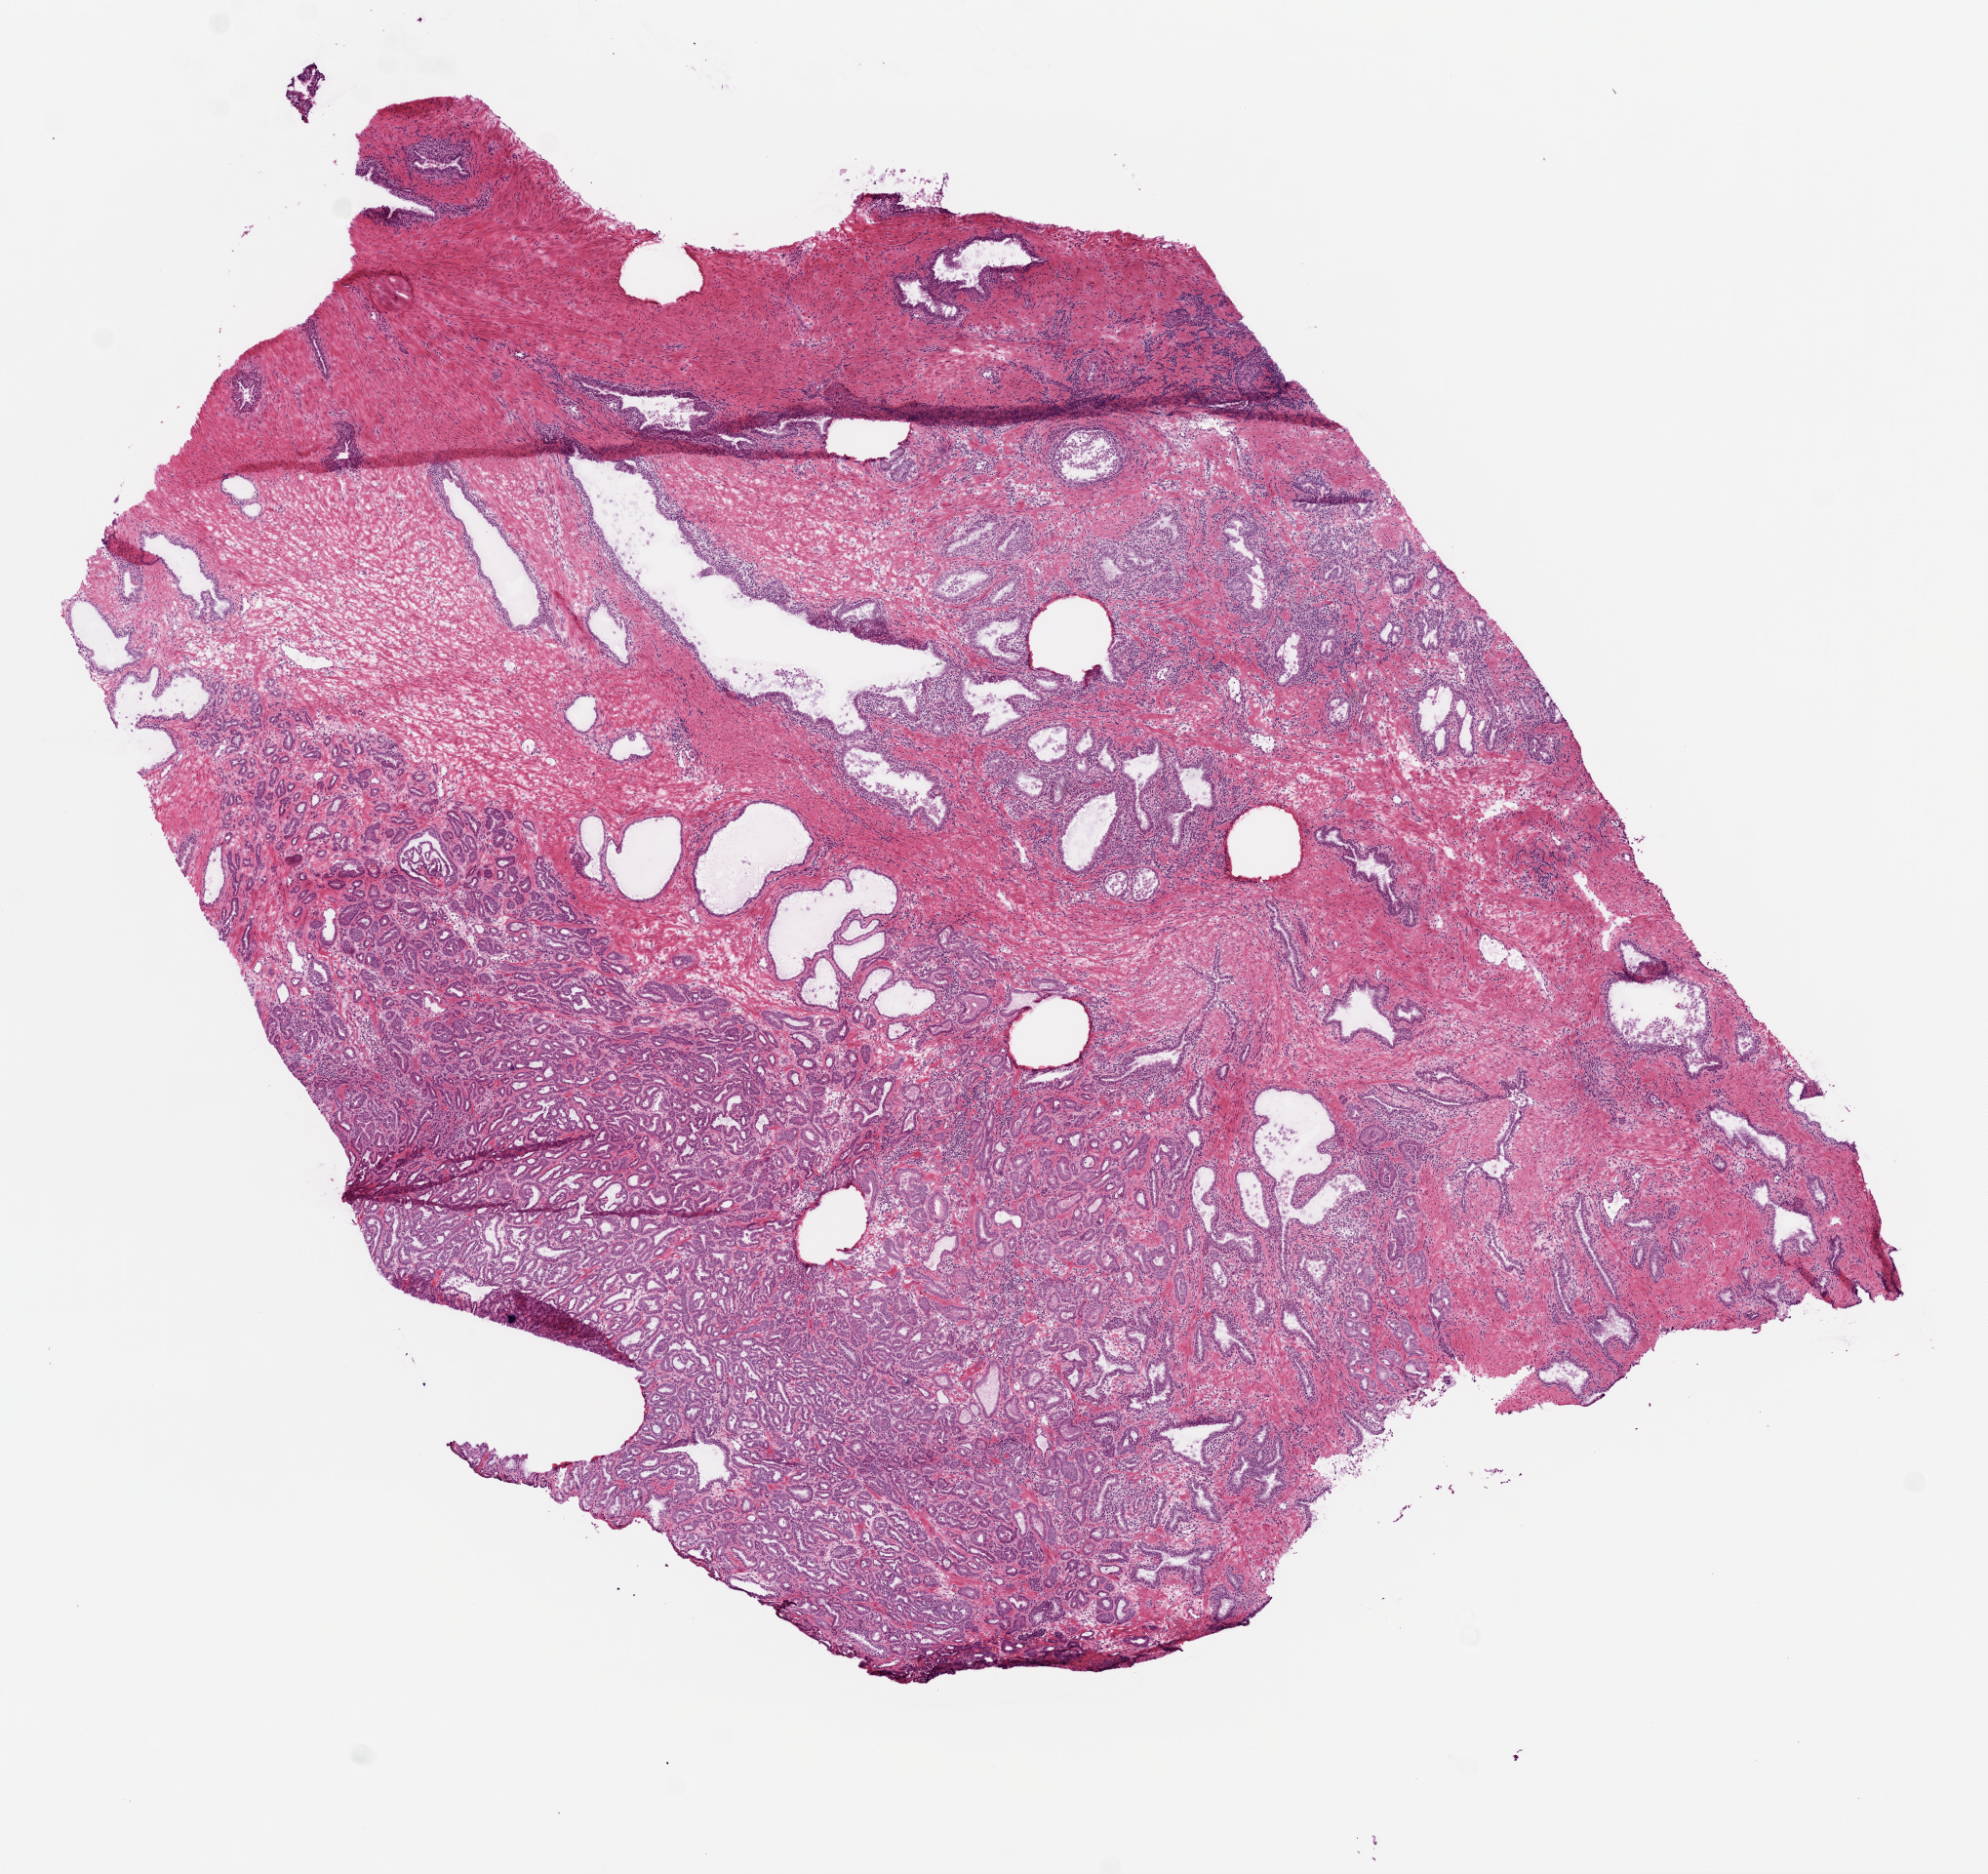
Whole-slide histology image, H&E, a low-resolution overview of the entire scanned area, about 8.2 x 7.7 mm, frozen section from the top of the tissue portion, prostate, primary tumour sample. Male, age 53 years at initial diagnosis. Gleason score: 7 (3+4). Composition of this section per pathologist review: tumour cells 90%, tumour nuclei 90%, normal cells 8%, stromal cells 2%, necrosis 0%.
Laterality: bilateral. Pathologic diagnosis: Acinar cell carcinoma (prostate gland).